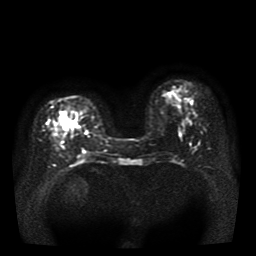
Breast MRI, one axial slice. Slice 14 of 41 in the series (ordered by position). Diffusion-weighted series; image 2 of 4 stored at this slice position (different b-values; order by instance number). 1.5 T. 5 mm slice thickness. 256 × 256 image matrix. Female patient.
Structures marked on this image (outlined manually by an expert reader):
- tumour on diffusion-weighted imaging: bounding box <61,114,80,134> (left, top, right, bottom; pixels)